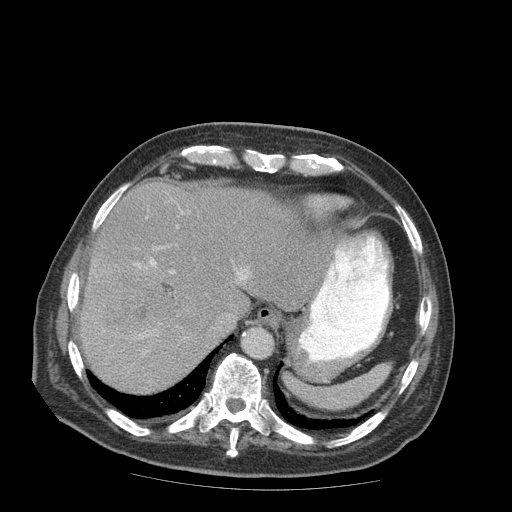
Contrast-enhanced abdominal CT (liver protocol), one axial slice; slice 69 of 99 in the series (ordered by position); soft-tissue window (W 400 / L 40 HU); 512 × 512 image matrix, field of view 420 × 420 mm. Case-level facts recorded for this patient, not image findings: diagnosis: hepatocellular carcinoma (patient treated with transarterial chemoembolisation; whether this scan precedes or follows treatment is not stated here); TNM stage (as recorded): Stage-IIIB.
Annotated regions visible in this slice (semi-automatic segmentation, software-assisted and operator-edited):
- liver parenchyma outside the tumour (the mass and vessels are separate outlines, so this box may not span the whole liver): box from (x=80, y=180) to (x=326, y=392) px
- mass: (x=94, y=270)–(x=173, y=337)
- liver vessels: (x=134, y=209)–(x=248, y=352)